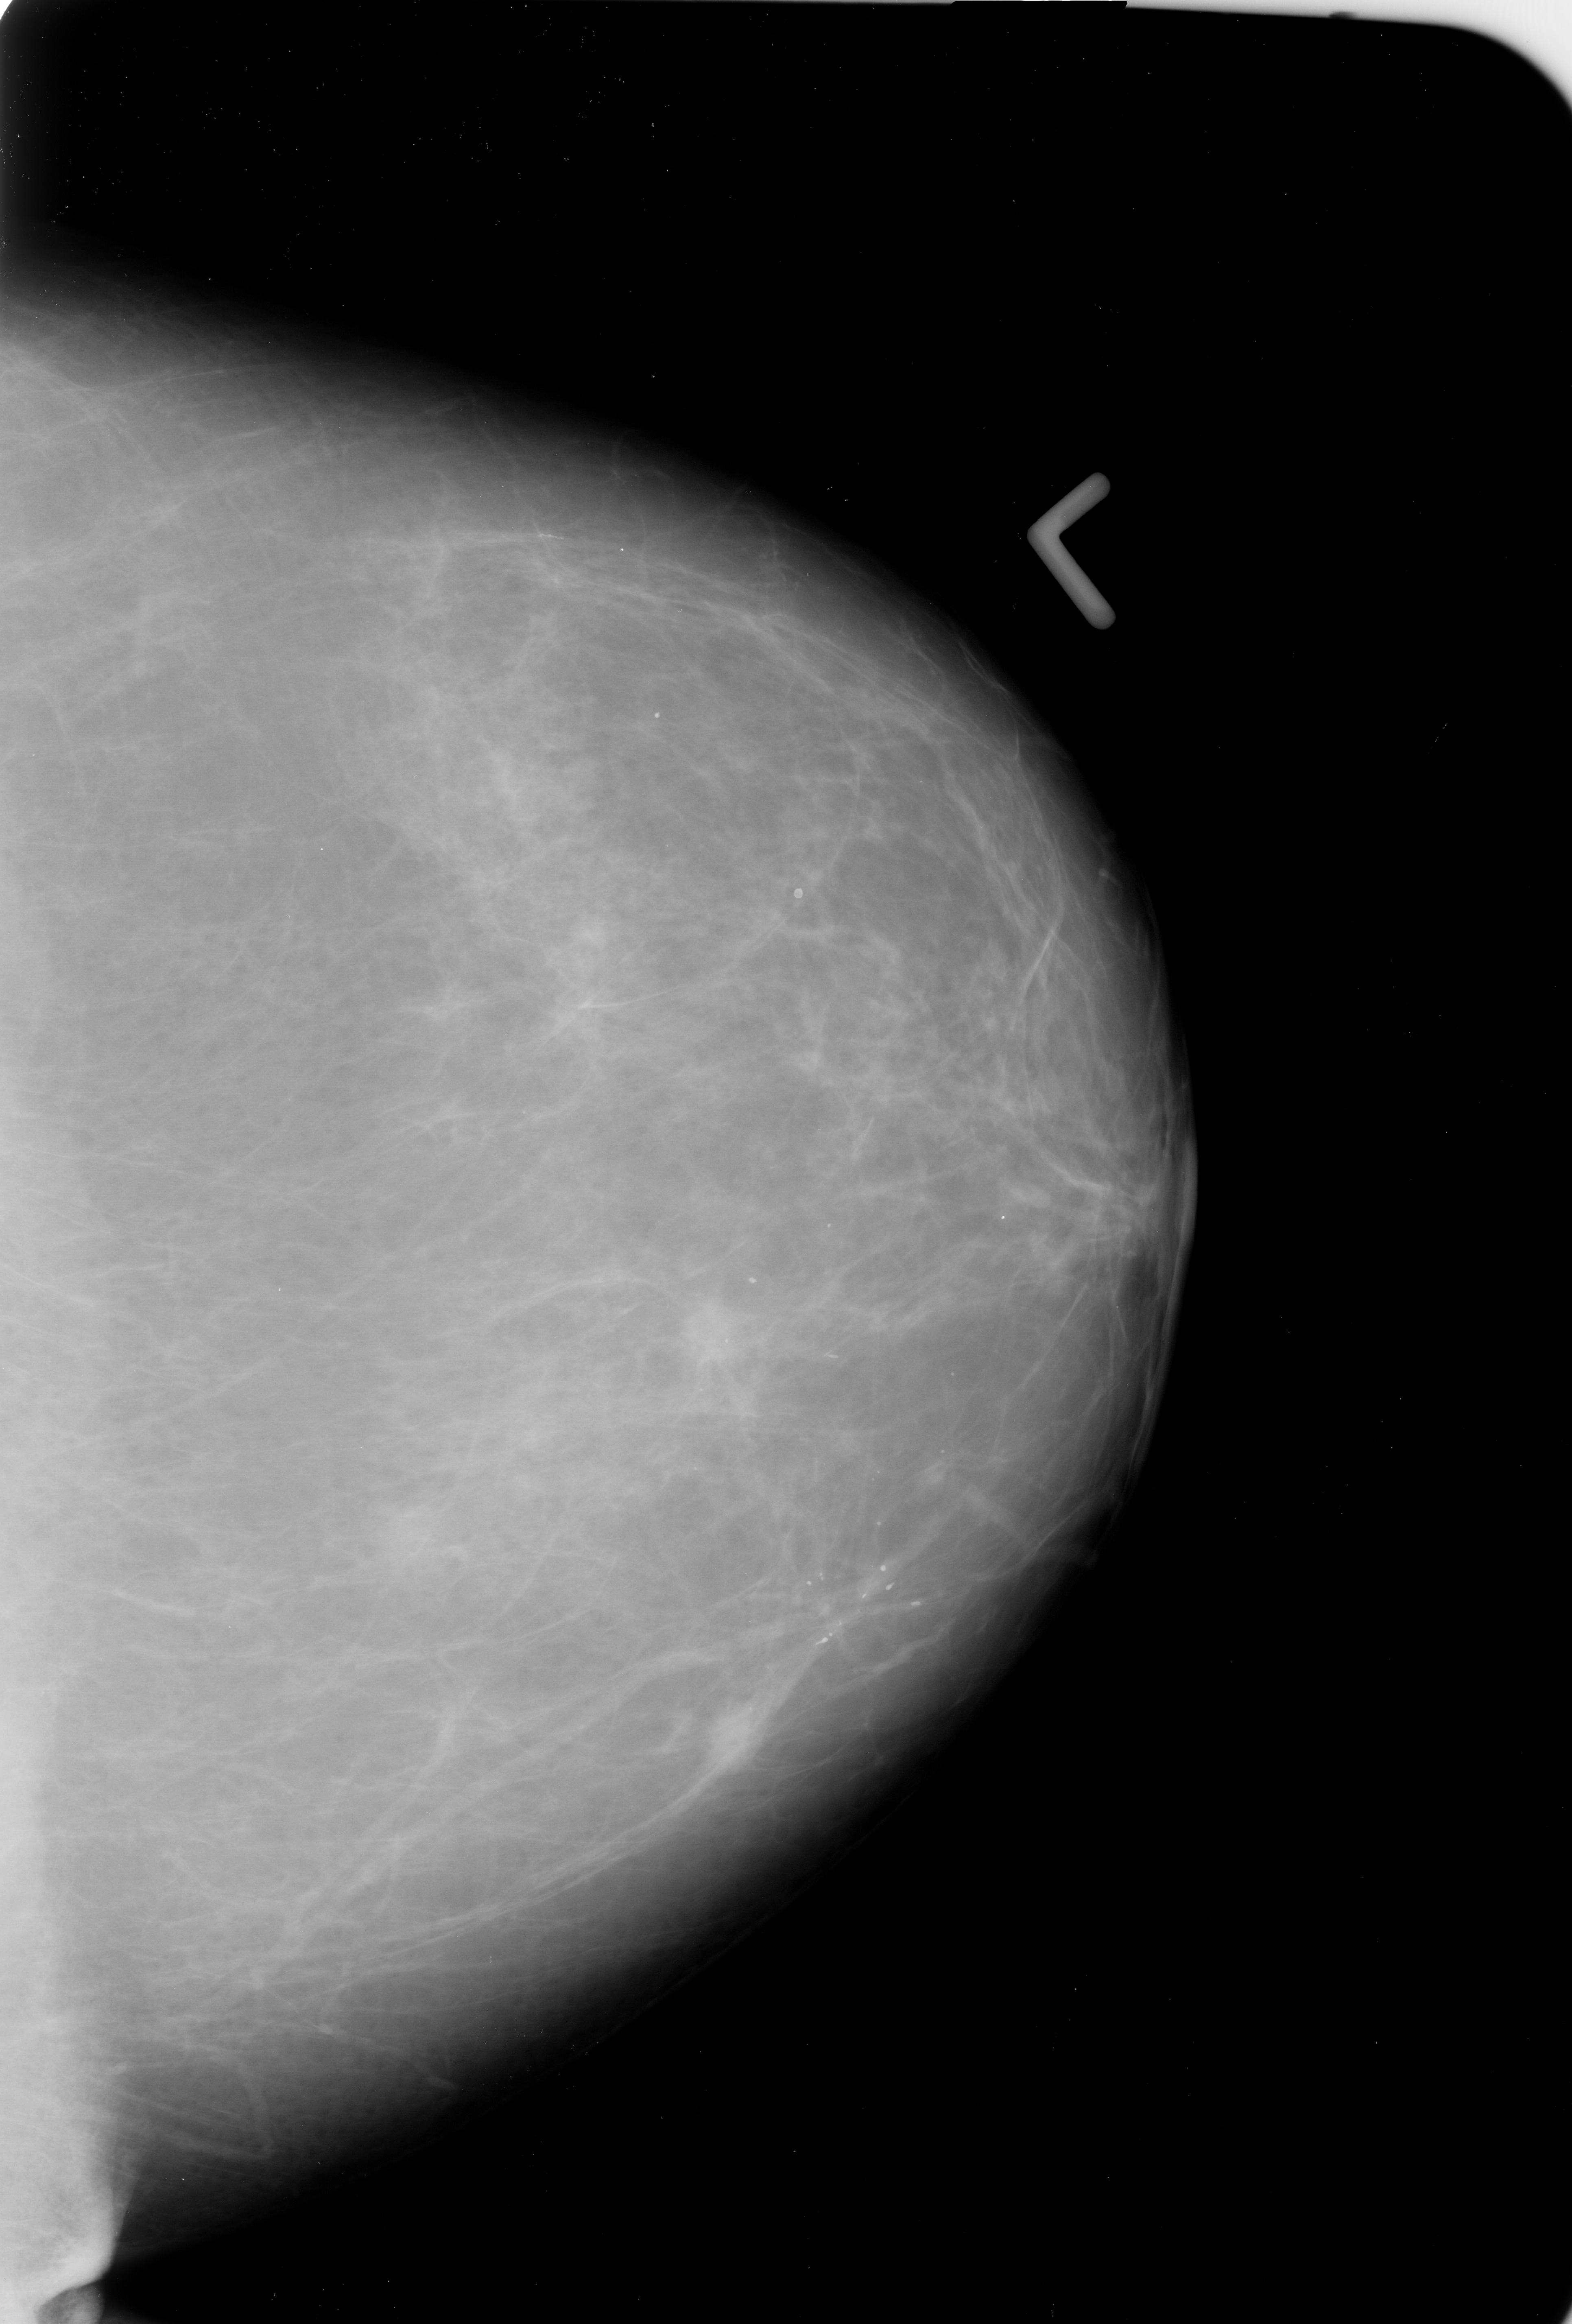
Scanned film-screen mammogram; left breast; craniocaudal (CC) view; breast composition: almost entirely fatty (BI-RADS density category 1 of 4).
Radiologist-marked abnormalities on this image: Finding 1 of 2: mass, shape irregular, margins spiculated; BI-RADS assessment category 4; subtlety rating 3 on a 1 (subtle) to 5 (obvious) scale; pathology result (as recorded, not read from the image): malignant. Finding 2 of 2: mass, shape irregular, margins spiculated; BI-RADS assessment category 4; subtlety rating 3 on a 1 (subtle) to 5 (obvious) scale; pathology result (as recorded, not read from the image): malignant.